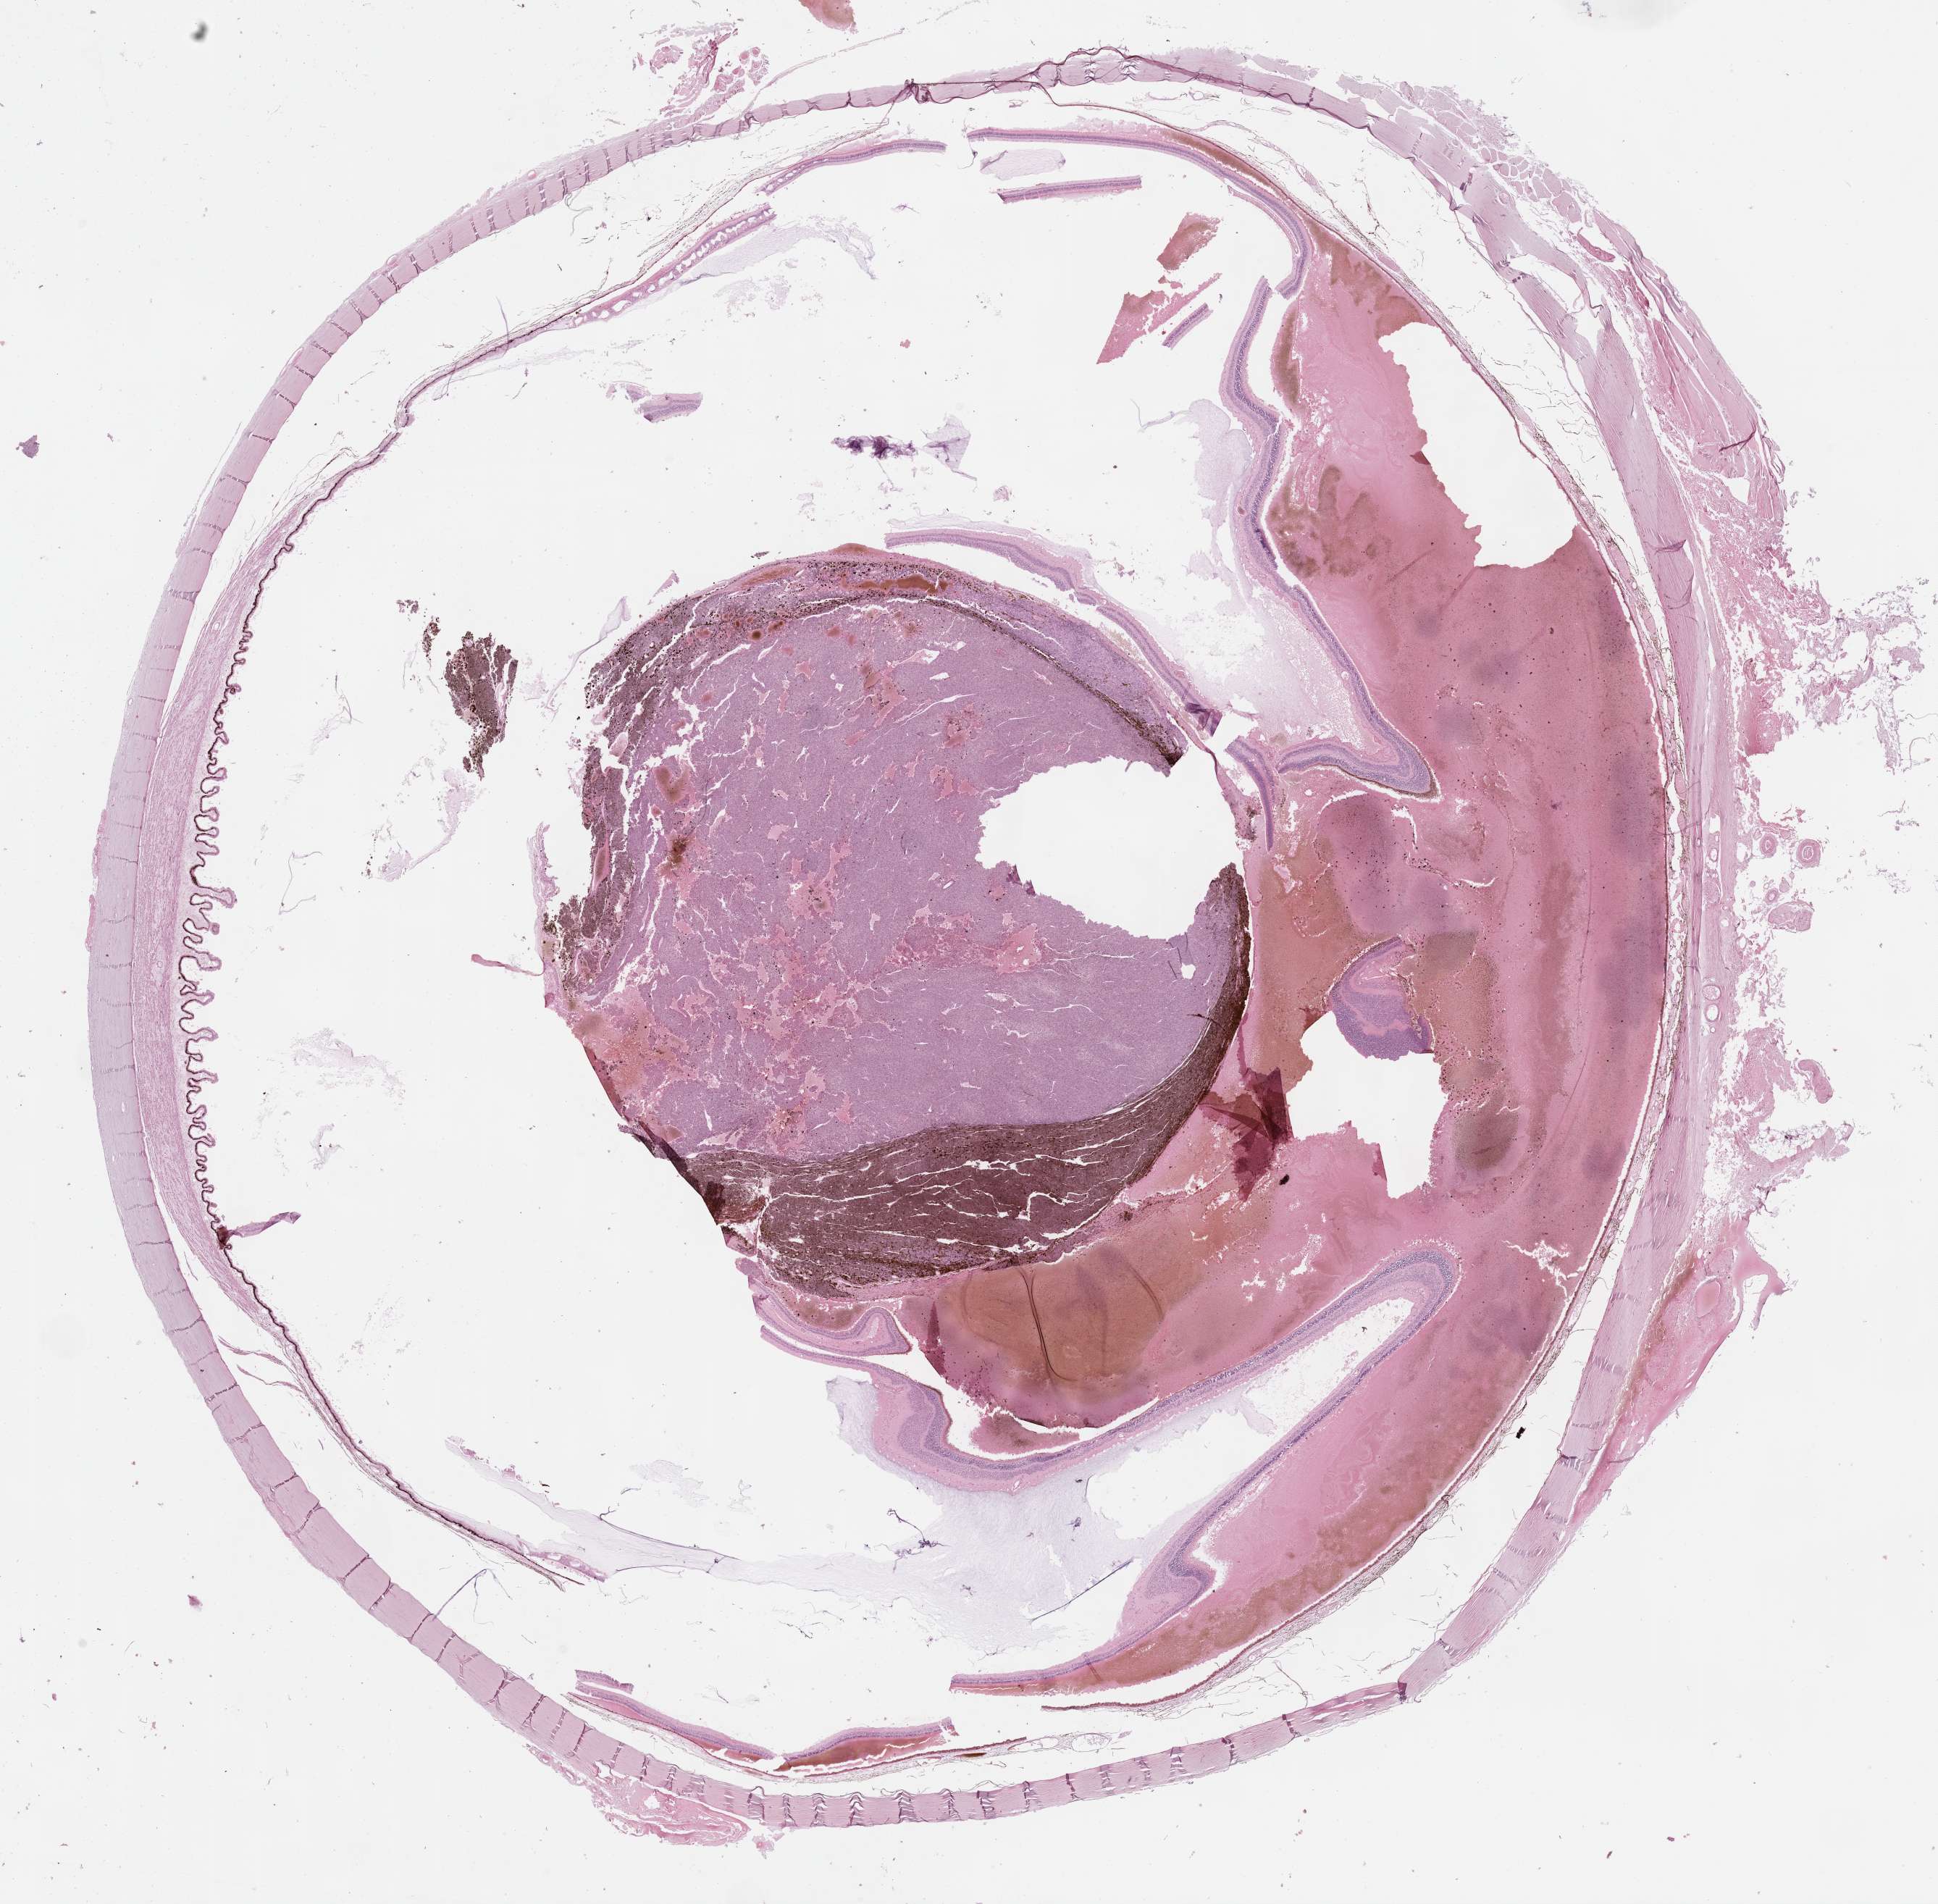
H&E whole-slide image — a low-resolution overview of the entire scanned area, about 21.6 x 21.3 mm (from a 40x scan). Formalin-fixed paraffin-embedded (FFPE) diagnostic section. Uvea, primary tumour sample. Male patient; age at initial diagnosis 68 years.
* histologic diagnosis: Mixed epithelioid and spindle cell melanoma (choroid)
* AJCC pathologic stage: IIIA (7th edition)
* TNM: T4a N0 M0